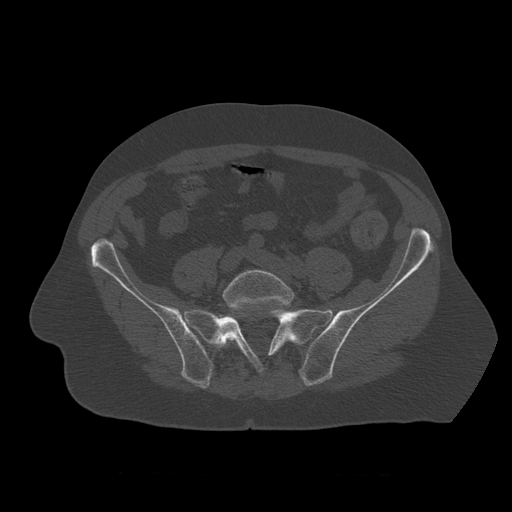
CT including the spine, one axial slice. Position 243 of 450 along the scan axis. Reconstruction kernel STANDARD. 120 kVp. Bone window (W 1800 / L 400 HU). 512 × 512 image matrix, field of view 405 × 405 mm. Patient age 75 years. Case-level facts recorded for this patient, not image findings: primary cancer: prostate.
Structures marked on this image (semi-automatically segmented with operator editing):
- L5 vertebra: box from (x=223, y=270) to (x=295, y=346) px